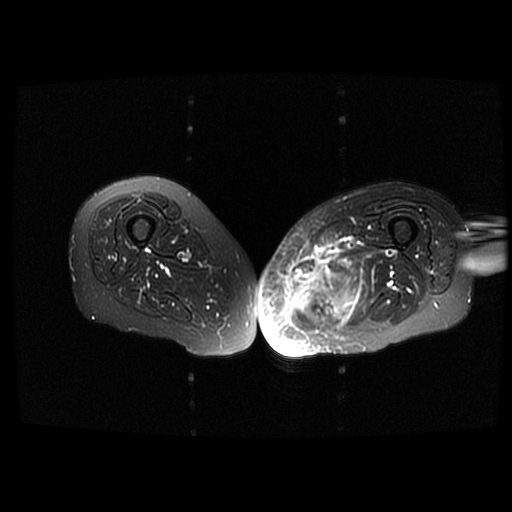
MRI of an extremity soft-tissue mass, one axial slice. T2-weighted fat-saturated. 6 mm slice thickness. 512 × 512 image matrix, field of view 420 × 420 mm. Female patient. From the clinical record (not read from this slice): histological type: pleomorphic leiomyosarcoma; grade: high; site of the primary tumour: left thigh.
Structures marked on this image (manually delineated by an expert):
- gross tumour volume including surrounding oedema: box from (x=287, y=249) to (x=360, y=334) px
- gross tumour volume (mass): (x=307, y=293)–(x=335, y=318)